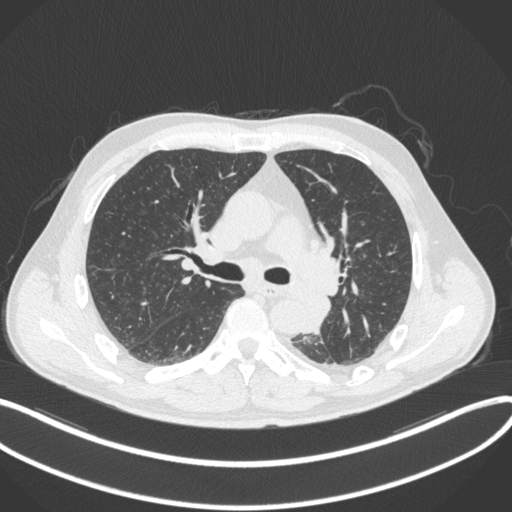
Chest CT, one axial slice. Reconstruction kernel B31f. 120 kVp. Lung window (W 1500 / L -600 HU). 1 mm slice thickness. 512 × 512 image matrix, field of view 400 × 400 mm. Male patient, age 59 years. From the clinical record (not read from this slice): clinical TNM (as recorded): T2a N2 M0.
Outlined on this slice (bounding box drawn by a radiologist):
- lung tumour (recorded histology: squamous cell carcinoma): bounding box (x1, y1, x2, y2) in pixels: (299, 286, 332, 338)